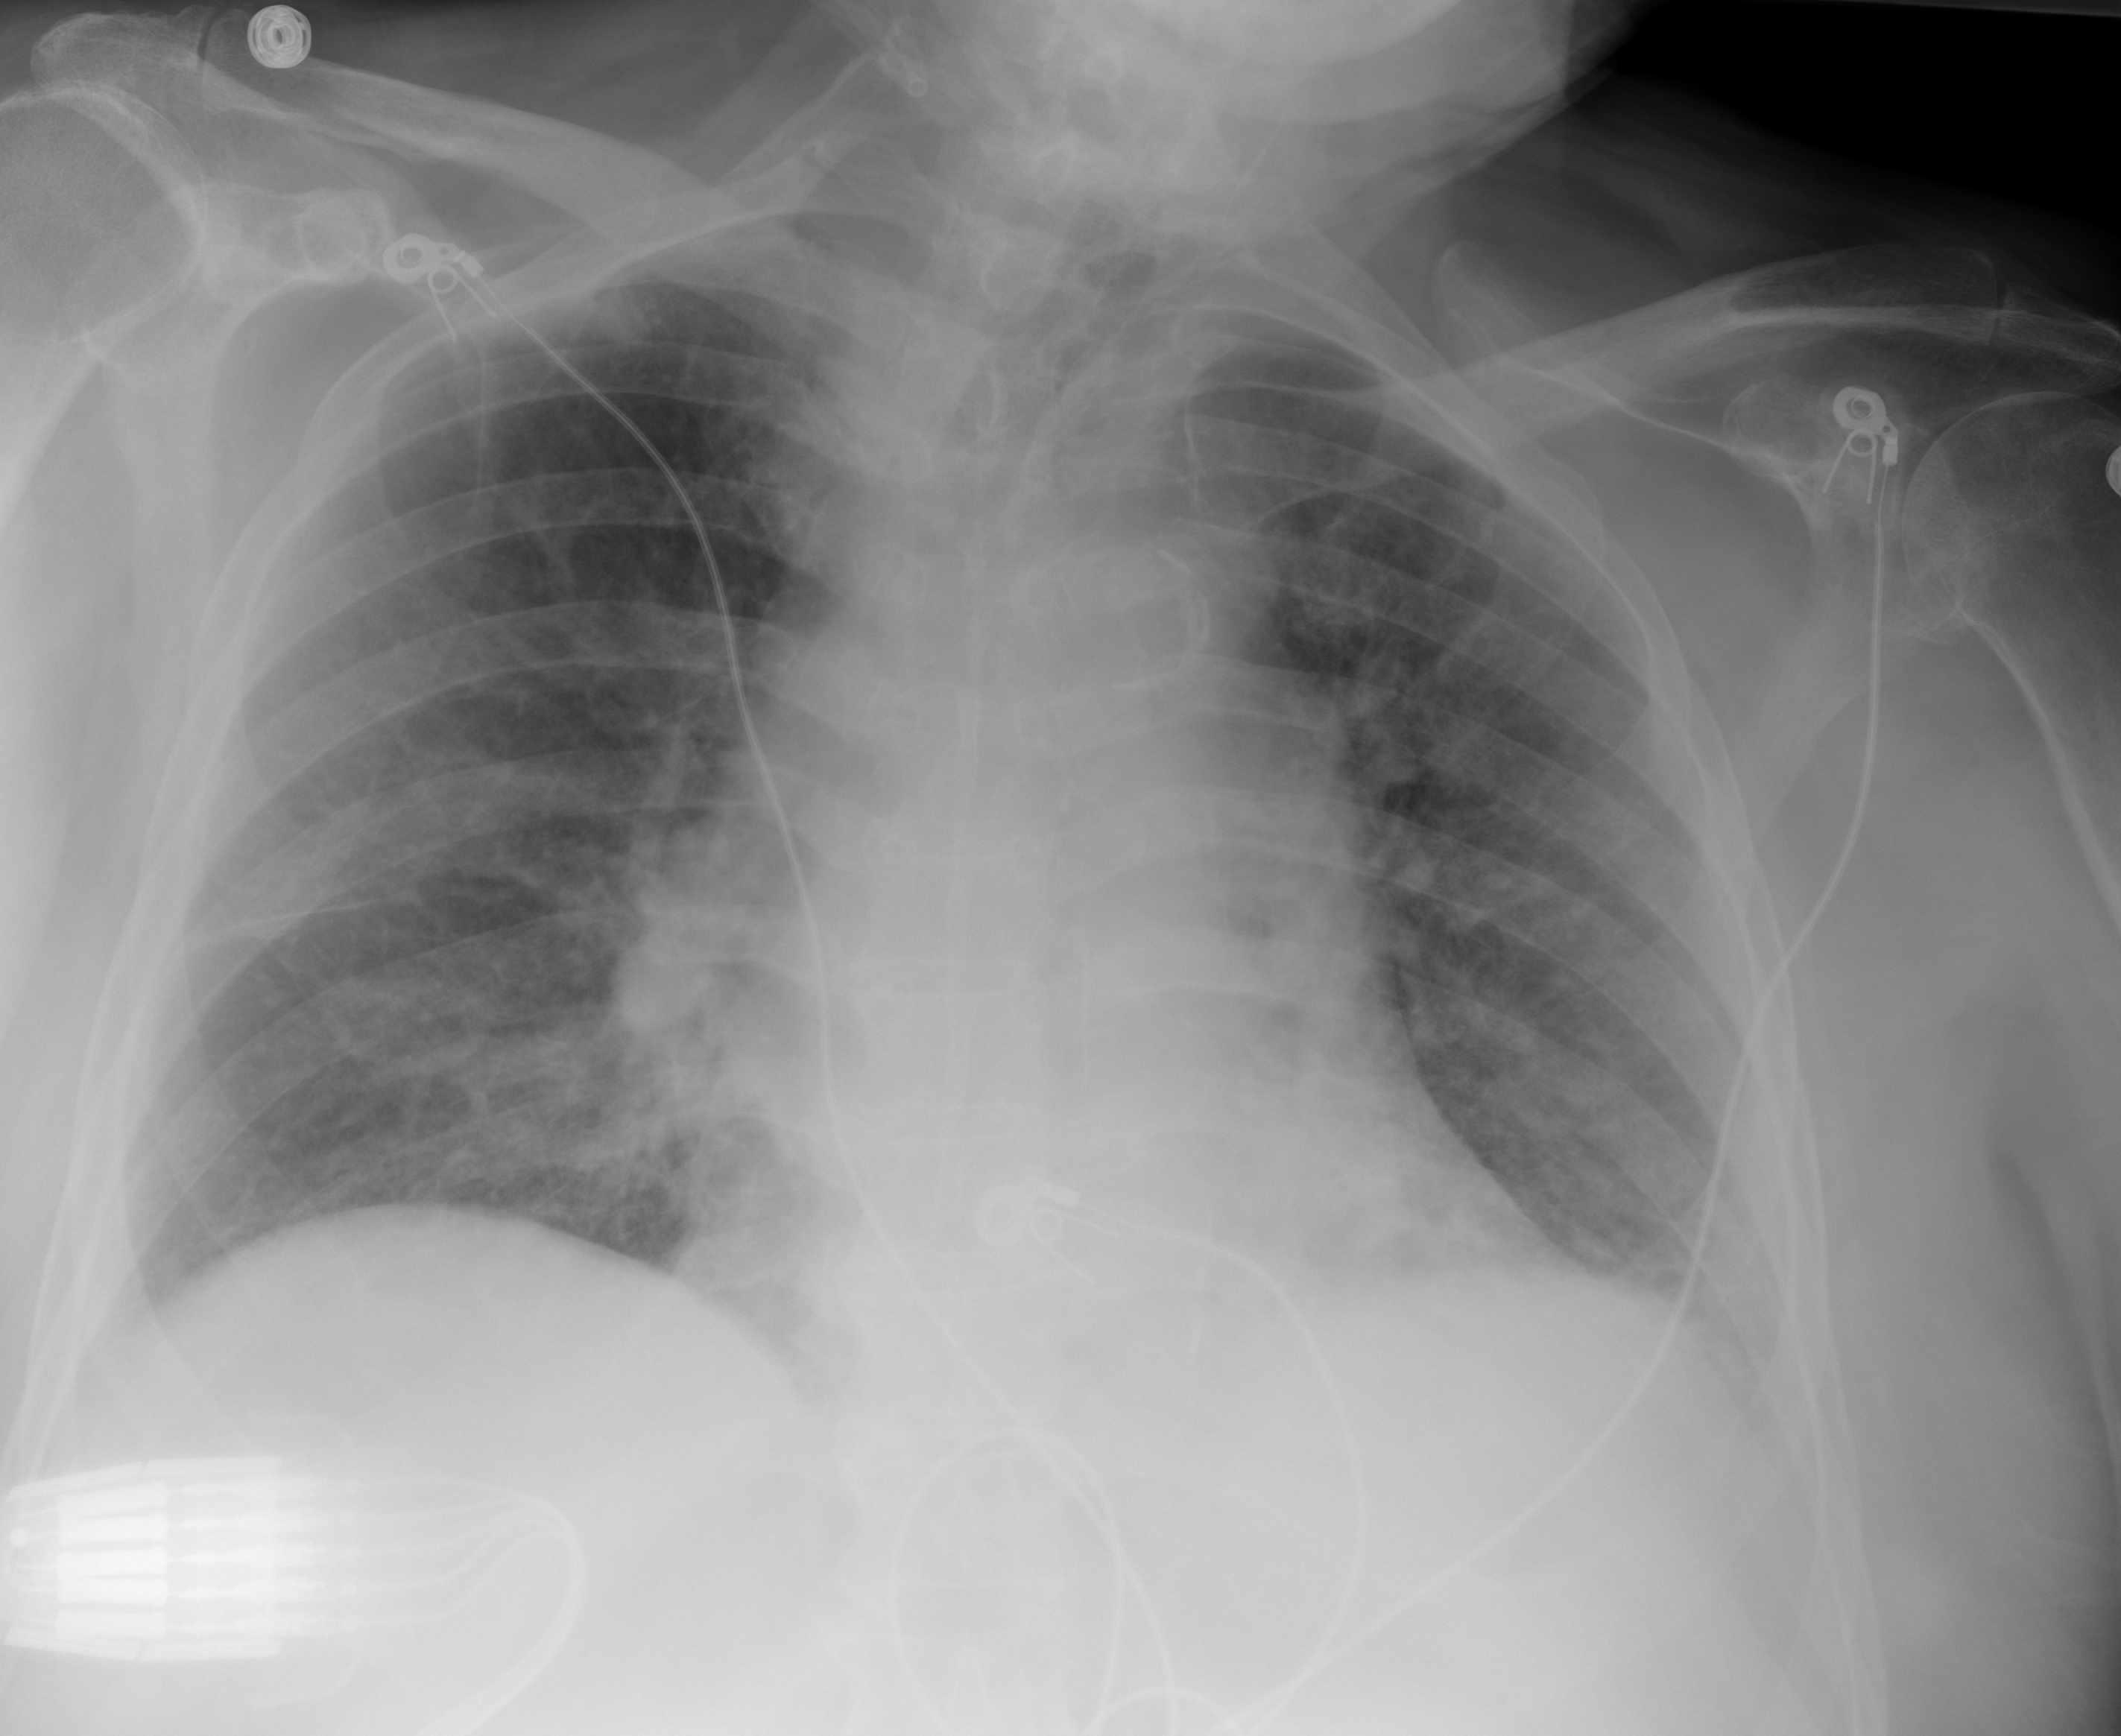
Chest X-ray (portable), AP projection. Male patient, age 89 years; imaged 0 days after the COVID-19 diagnosis.
Radiologist's key findings for this exam: subtle streaky opacities in the left lung base.